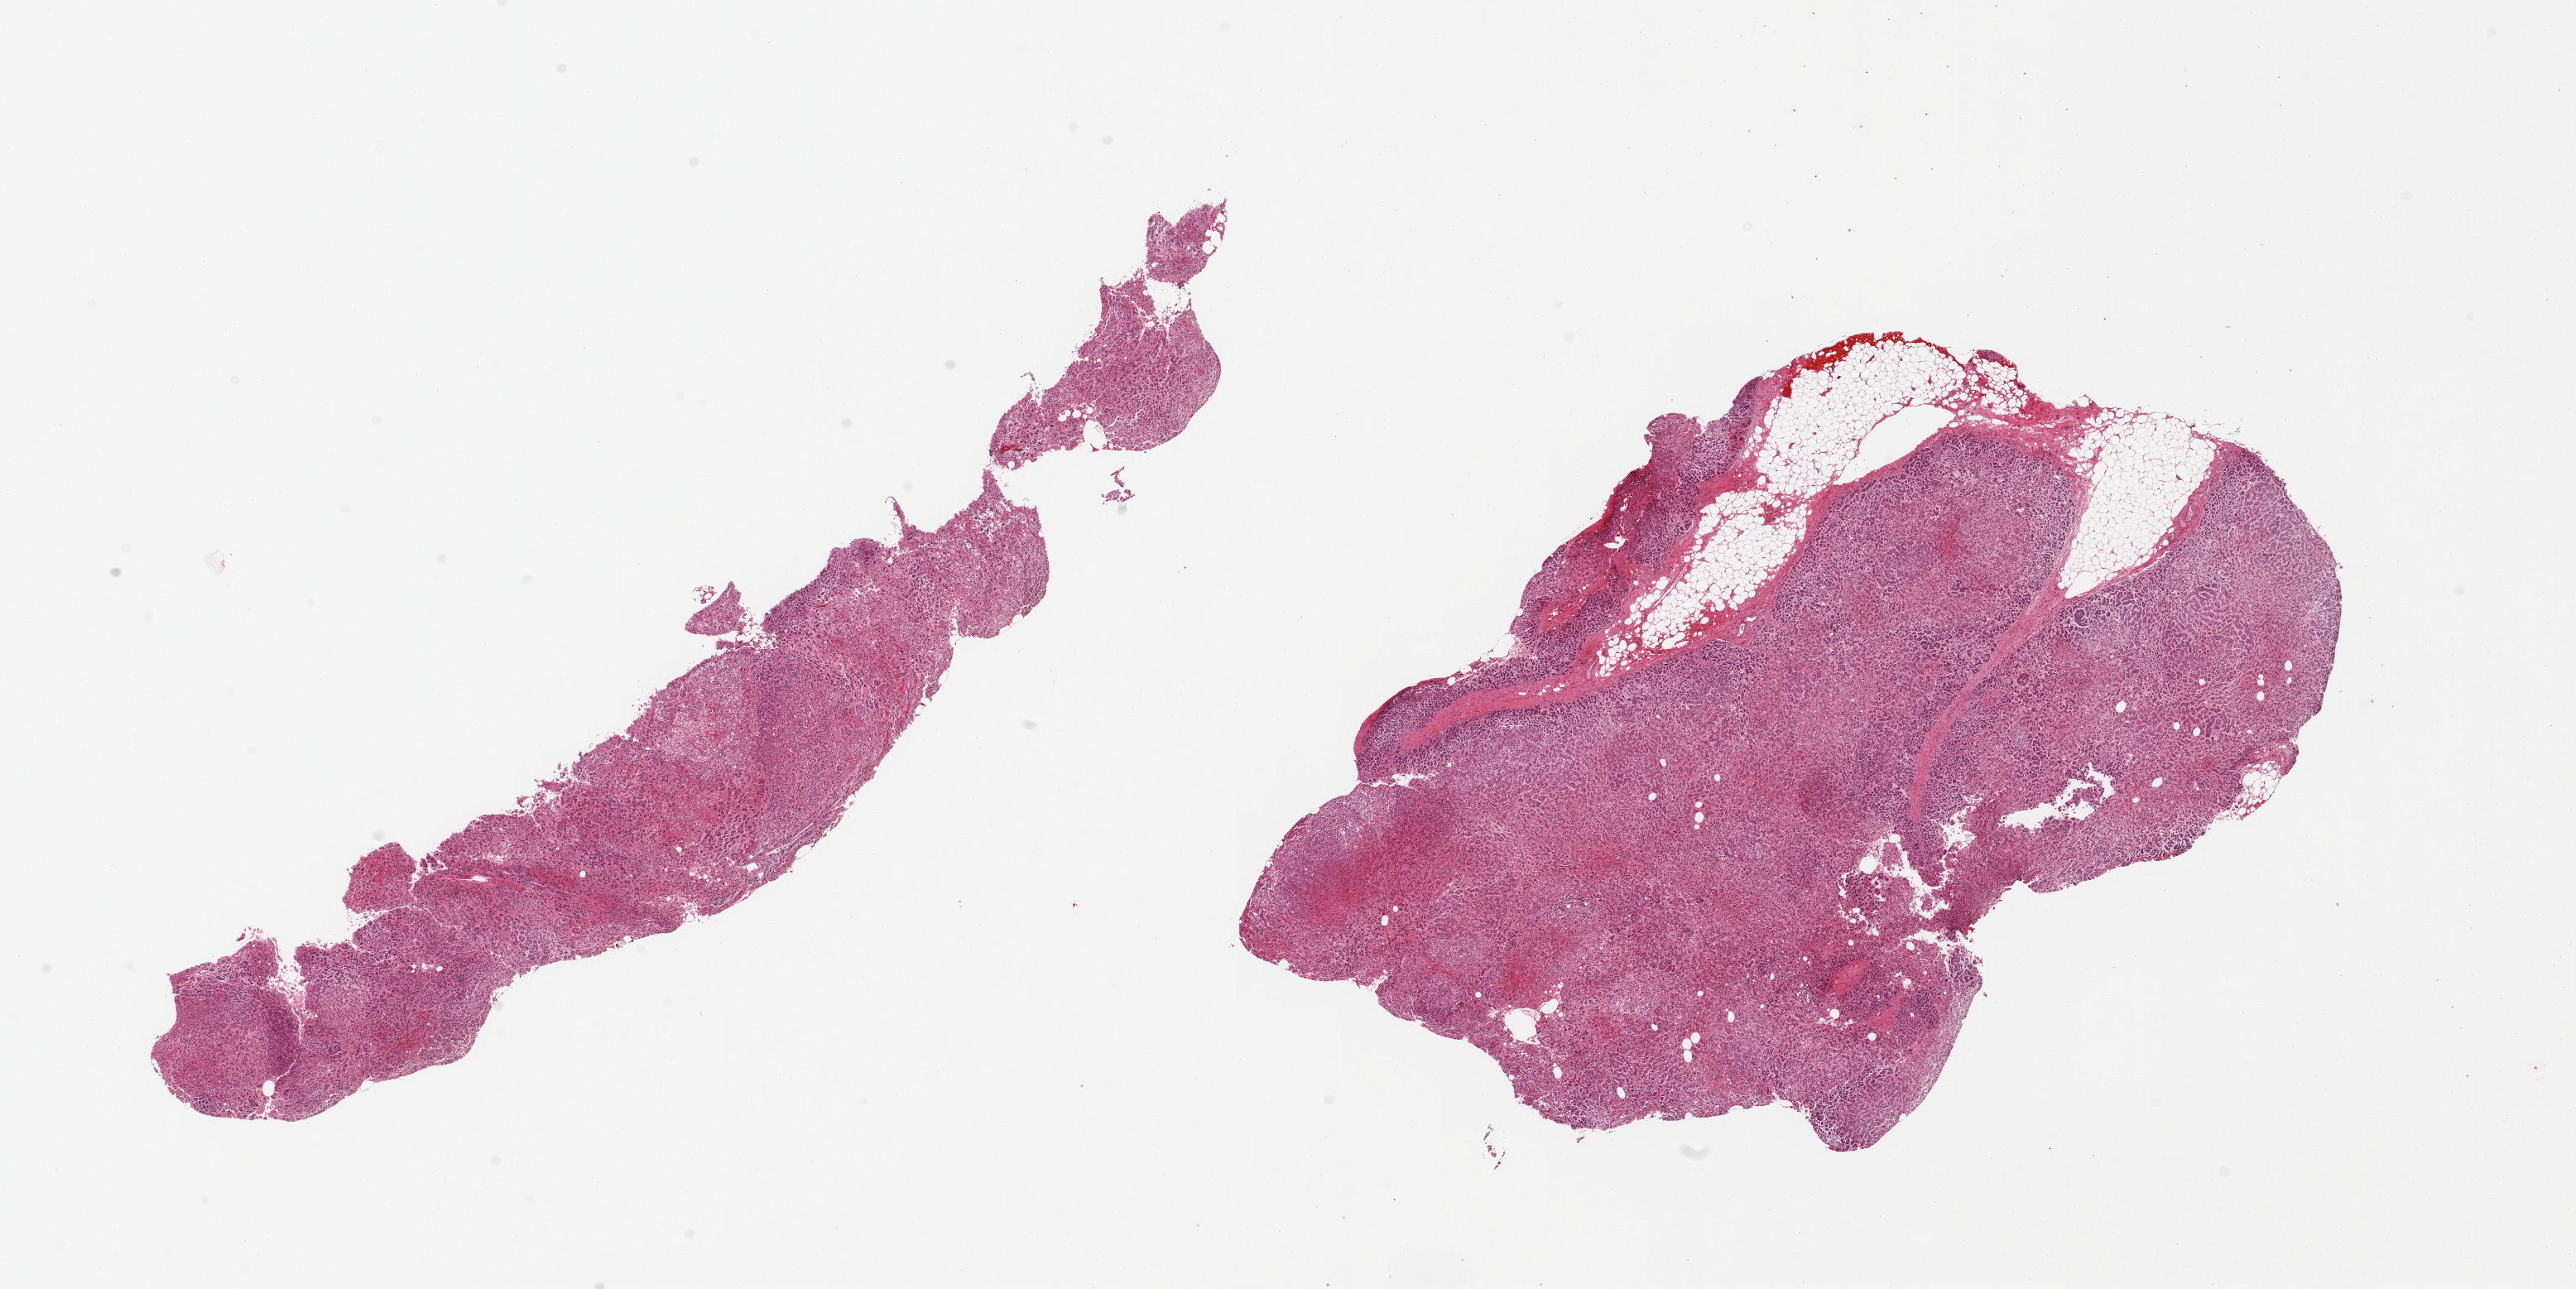
Whole-slide image, hematoxylin and eosin (H&E) stain, brightfield, a low-resolution overview of the entire scanned area, about 24.6 x 12.3 mm. PAXgene-fixed, paraffin-embedded tissue. Target tissue: adrenal gland. Tissue donor sample. Donor sex: female.
Pathologist's review note for this sample: 2 pieces; predominantly adrenal cortex with ~10% fat in one piece.